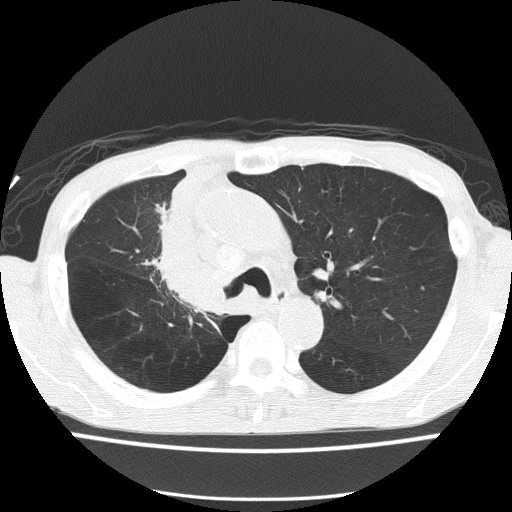
Axial slice from a low-dose chest CT screening exam; baseline screening round; lung window (W 1500 / L -600 HU); slice 49 of 150 in the series. Male, age 59 years at enrolment. Former smoker at enrolment.
- Lesion marked by an expert reader, bounding box (x1, y1, x2, y2) in pixels: (138, 231, 235, 322).
- The screening reader recorded 5 non-calcified nodules or masses ≥4 mm on this exam (left upper lobe, left upper lobe, left upper lobe, right middle lobe, right lower lobe); which of them this box marks is not recorded.
- Official screen result: positive, change unspecified: nodule(s) >= 4 mm or enlarging nodule(s), mass(es), or other non-specific abnormalities suspicious for lung cancer.
- Lung cancer was diagnosed 72 days after this screen: squamous cell carcinoma, NOS, right upper lobe, moderately differentiated (G2), stage IV (AJCC 6th edition).